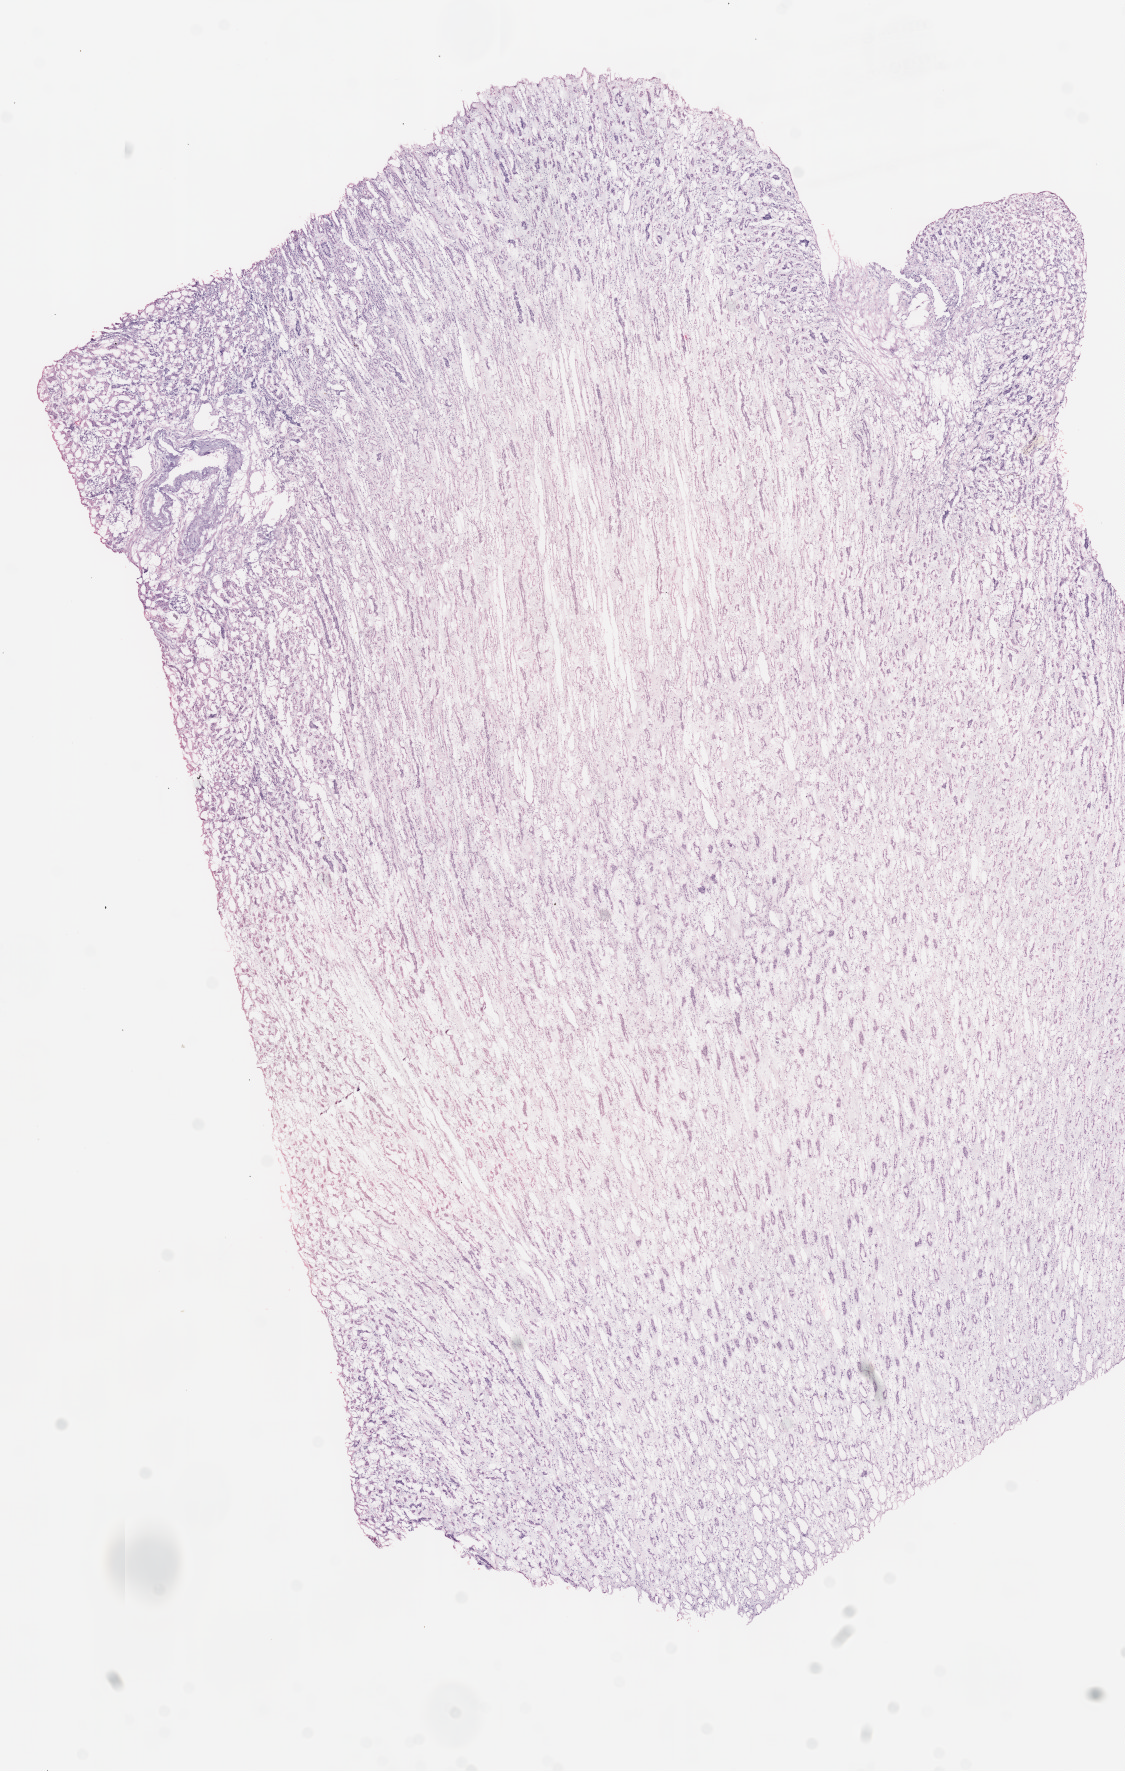
Digitized H&E tissue section (whole slide) — low-resolution overview of the scanned area, about 9.0 x 14.2 mm (from a 20x scan). Frozen section from the top of the tissue portion. Kidney, solid tissue normal (non-tumour tissue) sample. Male, age 67 years at initial diagnosis.
• this section: solid tissue normal (non-tumour) sample from the same patient
• patient diagnosis: Clear cell adenocarcinoma, NOS